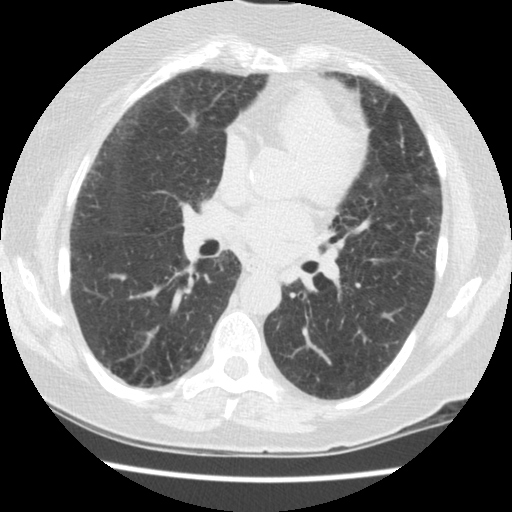
Chest CT (low-dose screening protocol), one axial image. Second screening round (one year after baseline). Lung window (W 1500 / L -600 HU). 2.5 mm slice thickness. Slice 66 of 134 in the series. Female participant, aged 60 years at enrolment.
Expert reader's lesion annotation, bounding box <271,254,317,299> (left, top, right, bottom; pixels). The exam's reader record, not a measurement of the box and not confirmed to be the same lesion: non-calcified nodule or mass ≥4 mm, left lower lobe, 5 × 4 mm, smooth margins, soft tissue attenuation, pre-existing on the prior screen: yes; interval growth: no. Lung cancer was diagnosed 423 days after this screen: small cell carcinoma, NOS, left lower lobe, undifferentiated (G4), stage IV (AJCC 6th edition), 69 mm at pathology.